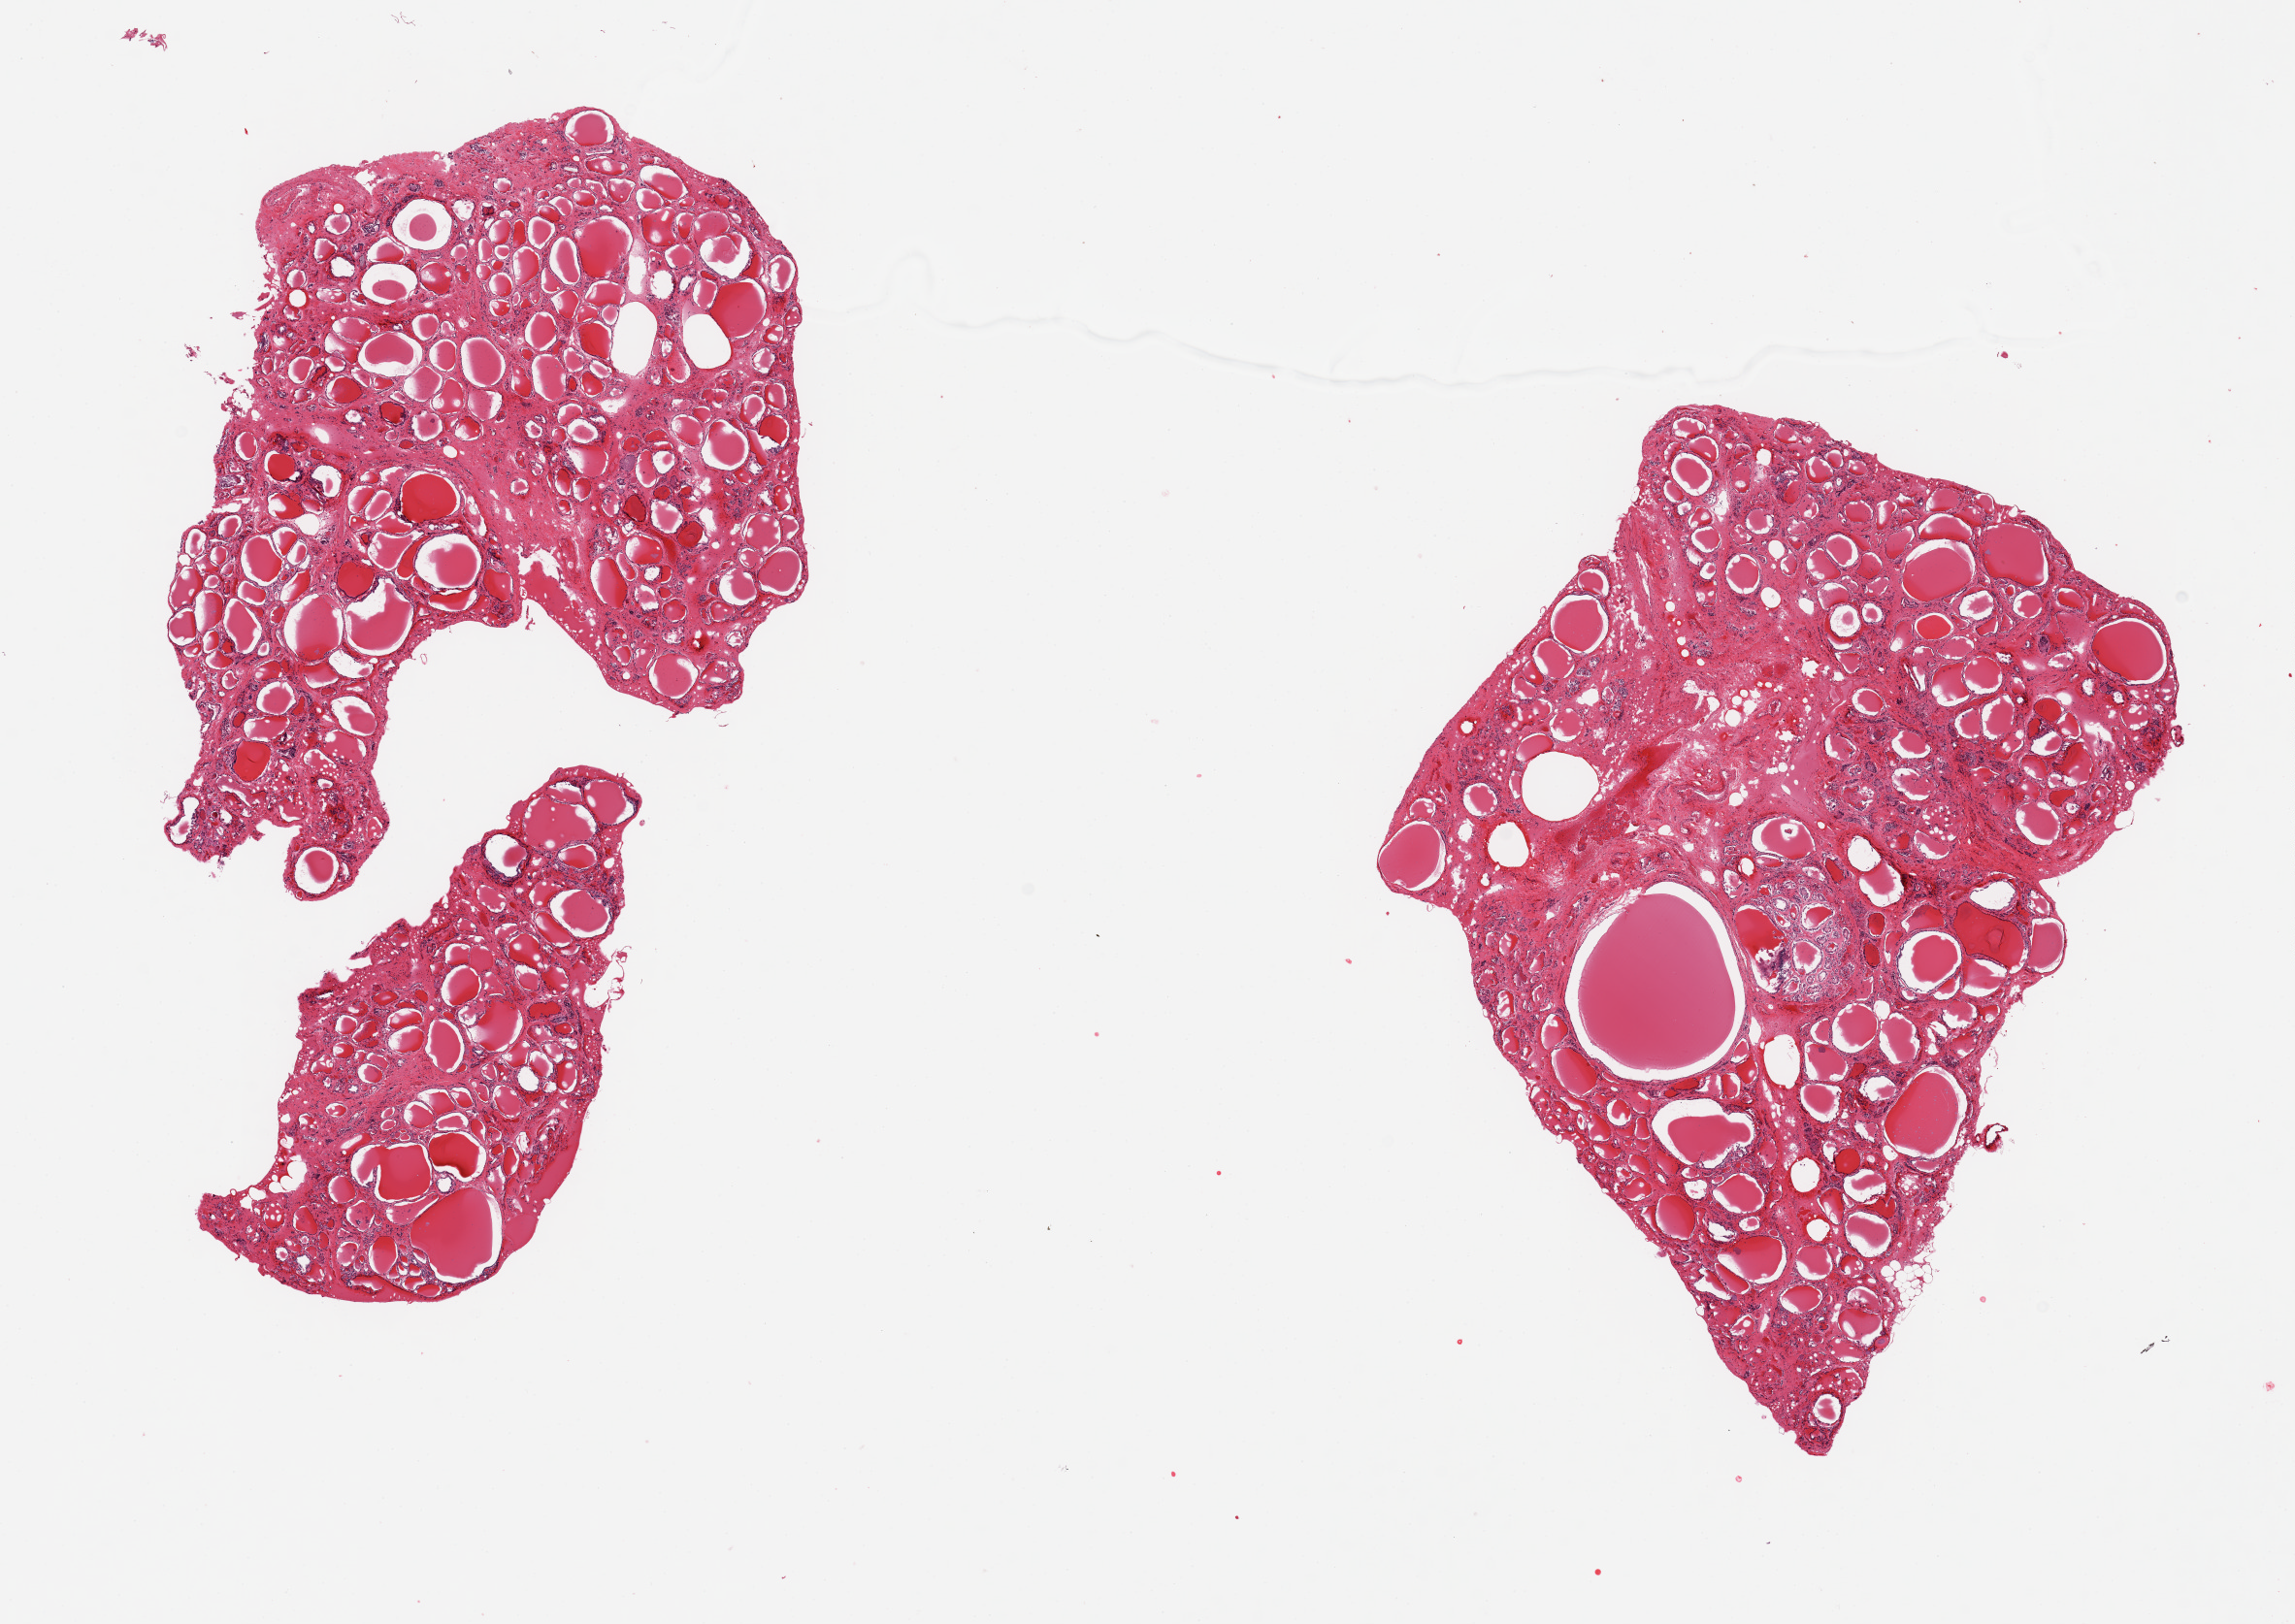
Whole-slide image, H&E stain, shown as a low-resolution overview of the whole scanned area (about 18.7 x 13.2 mm), PAXgene-fixed paraffin-embedded (PFPE) section, sampled site (target tissue): thyroid, donor tissue sample. Donor sex: male.
Review note (as recorded): 2 pieces, colloid cysts up to ~1.5mm.